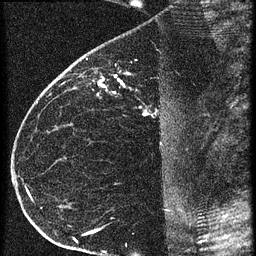
Breast MRI (dynamic contrast-enhanced), one sagittal slice. Position 37 of 60 along the scan axis. 3 images stored at this slice position (order not interpretable as contrast timing). 1.5 T. TE 4.2 ms, TR 20.4 ms. 1.5 mm slice thickness. 256 × 256 image matrix, field of view 180 × 180 mm. Patient: female, 35 years. From the clinical record (not read from this slice): setting: breast cancer imaged before/during neoadjuvant chemotherapy; receptor status: HR-positive, HER2-negative.
Annotated regions visible in this slice (semi-automatic segmentation, software-assisted and operator-edited):
- analysis volume of interest (the breast-tissue region the enhancement analysis was run in; not a lesion): bounding box [x1, y1, x2, y2] px = [65, 60, 169, 119]
- tumour enhancement mask (voxels above the 90 % enhancement threshold inside the analysis volume of interest): [98, 74, 149, 115]